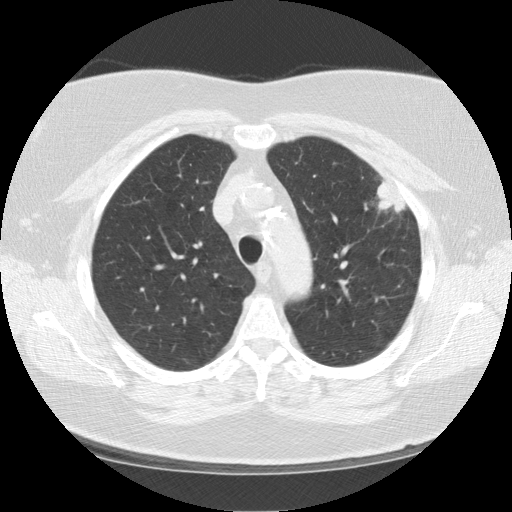
Low-dose screening chest CT, one axial slice; slice 99 of 130 in the series (ordered by position); lung window (W 1500 / L -600 HU); 2.5 mm slice thickness; 512 × 512 image matrix, field of view 350 × 350 mm.
Outlined on this slice (outlined manually by an expert reader):
- lesion 1 (tumor, upper lobe of left lung): box from (x=377, y=181) to (x=408, y=213) px